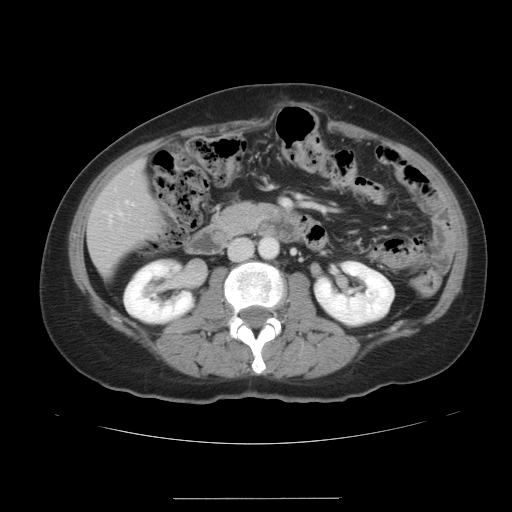
Contrast-enhanced abdominal CT, one axial slice. Position 12 of 41 along the scan axis. 120 kVp. Intravenous contrast given. Soft-tissue window (W 400 / L 40 HU). 5 mm slice thickness. 512 × 512 image matrix, field of view 381 × 381 mm. Female patient, age 63 years. Case-level facts recorded for this patient, not image findings: diagnosis: colorectal cancer liver metastases, imaged before liver resection; multiple liver metastases: yes; largest metastasis: 1.5 cm.
Structures marked on this image (outlined manually by an expert reader):
- liver: box from (x=89, y=162) to (x=162, y=275) px
- planned liver remnant (the part of the liver to remain after resection): (x=89, y=168)–(x=162, y=275)